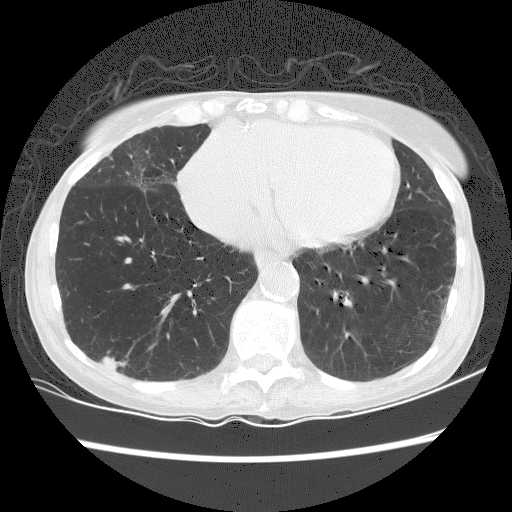
Low-dose screening chest CT, one axial slice; slice 62 of 156 in the series (ordered by position); 120 kVp; lung window (W 1500 / L -600 HU); 512 × 512 image matrix.
Outlined on this slice (expert manual segmentation):
- lesion 1 (tumor, lower lobe of right lung): bounding box (x1, y1, x2, y2) in pixels: (102, 351, 127, 370)